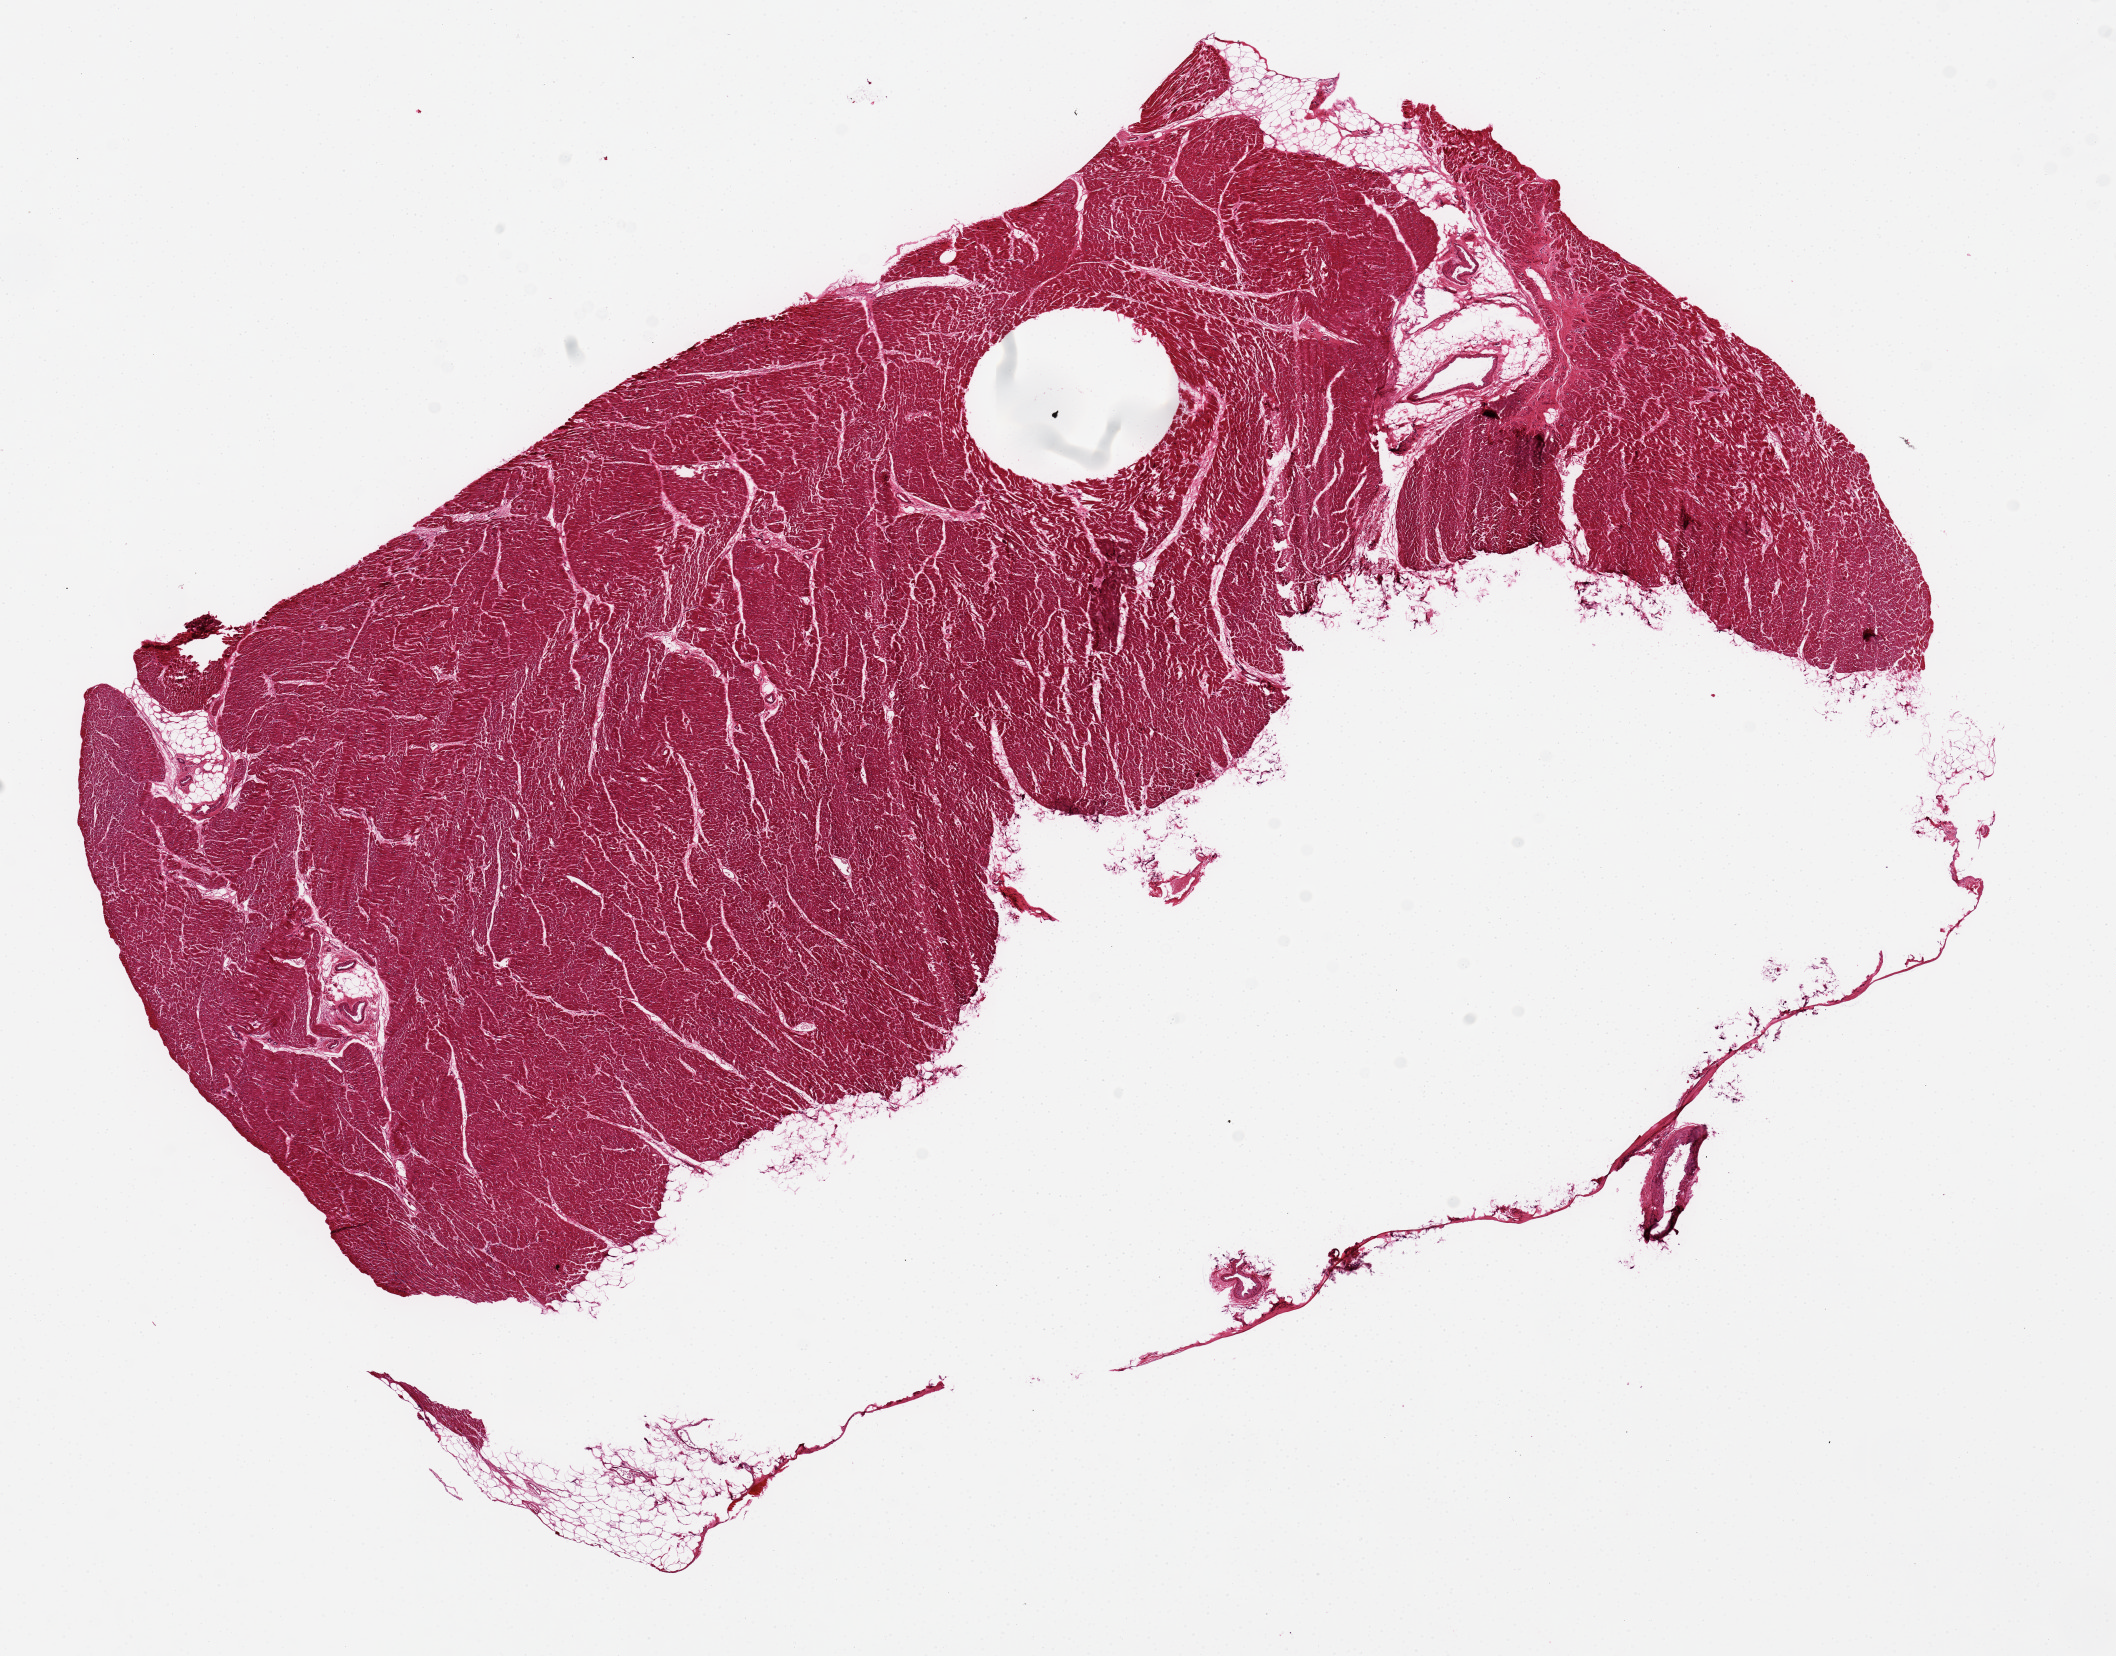
Haematoxylin and eosin whole-slide image — whole scanned area (about 16.7 x 13.1 mm) shown as a low-resolution overview; PAXgene-fixed, paraffin-embedded tissue; sampled site (target tissue): heart; tissue donor sample. Donor: male.
Pathologist's review note for this sample: Pericardial fat layer poorly fixed. 13x5.6mm. Possible early ischemia.